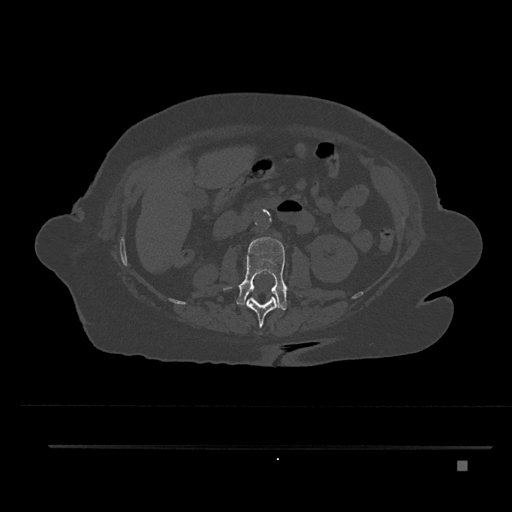
CT including the spine, one axial slice. Reconstruction kernel Br40s/3. Bone window (W 1800 / L 400 HU). 0.5 mm slice thickness. 512 × 512 image matrix, field of view 437 × 437 mm. Female patient, age 76 years. Case-level facts recorded for this patient, not image findings: primary cancer: lung.
Outlined on this slice (semi-automatic segmentation, software-assisted and operator-edited):
- L1 vertebra: bounding box (x1, y1, x2, y2) in pixels: (246, 297, 279, 328)
- L2 vertebra: (224, 236, 287, 311)